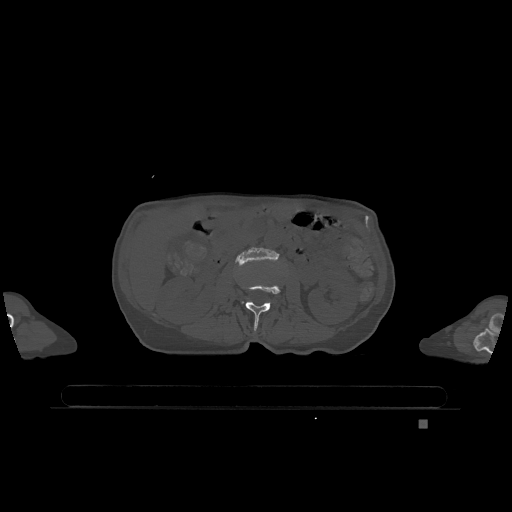
CT including the spine, one axial slice. Position 400 of 1317 along the scan axis. Bone window (W 1800 / L 400 HU). 0.5 mm slice thickness. 512 × 512 image matrix, field of view 500 × 500 mm. Patient: female, 74 years. Case-level facts recorded for this patient, not image findings: primary cancer: lung; vertebrae with lytic lesions (as recorded): T1, T4, T5, T6, L4, L5.
Annotated regions visible in this slice (semi-automatically segmented with operator editing):
- L2 vertebra: bounding box <243,284,281,330> (left, top, right, bottom; pixels)
- L3 vertebra: <236,247,279,265>